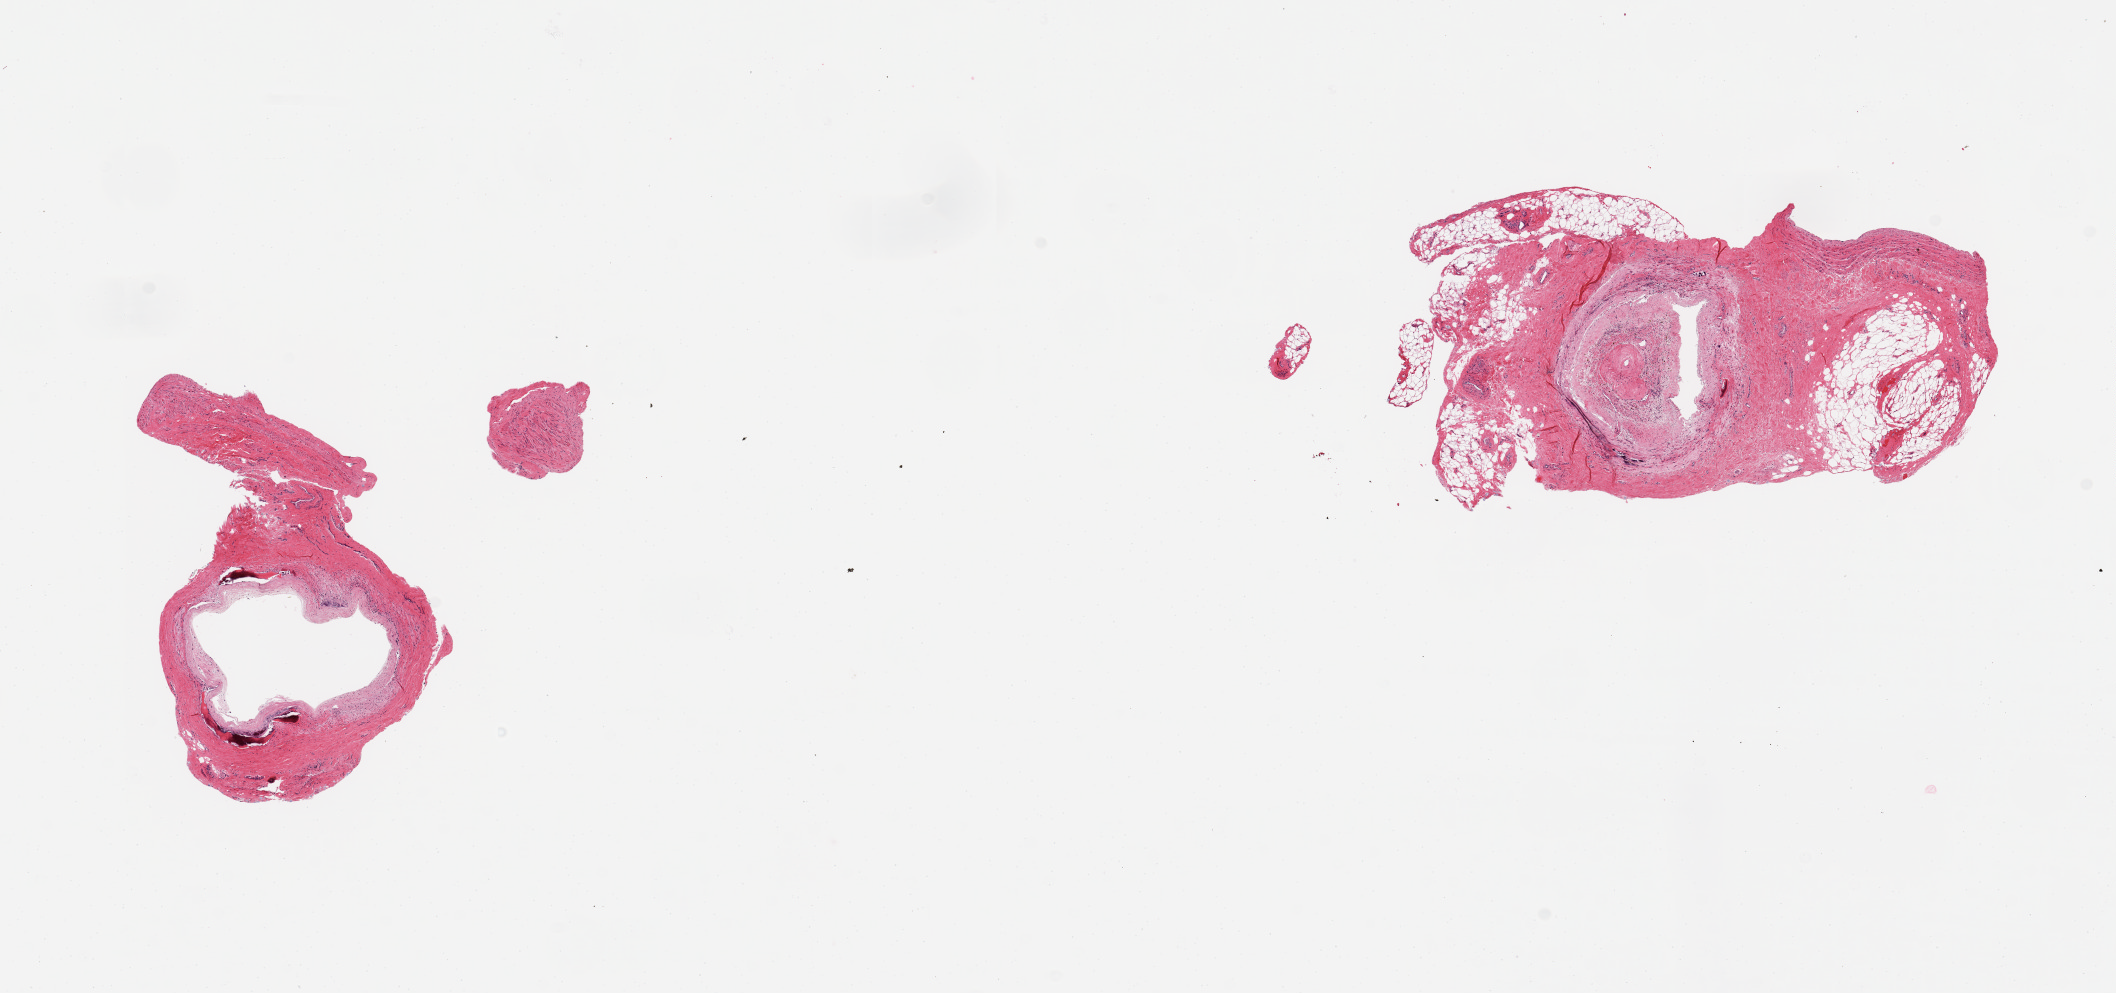
Whole-slide image, H&E stain, brightfield, shown as a low-resolution overview of the whole scanned area (about 16.7 x 7.9 mm). PAXgene-fixed, paraffin-embedded tissue. Sampled site (target tissue): tibial artery. Donor tissue sample. Donor sex: male.
* pathologist's review note for this sample: 2 pieces; severely sclerotic, calcified, ossified plaques; 1 with 60% extraneous fibrofatty tissue